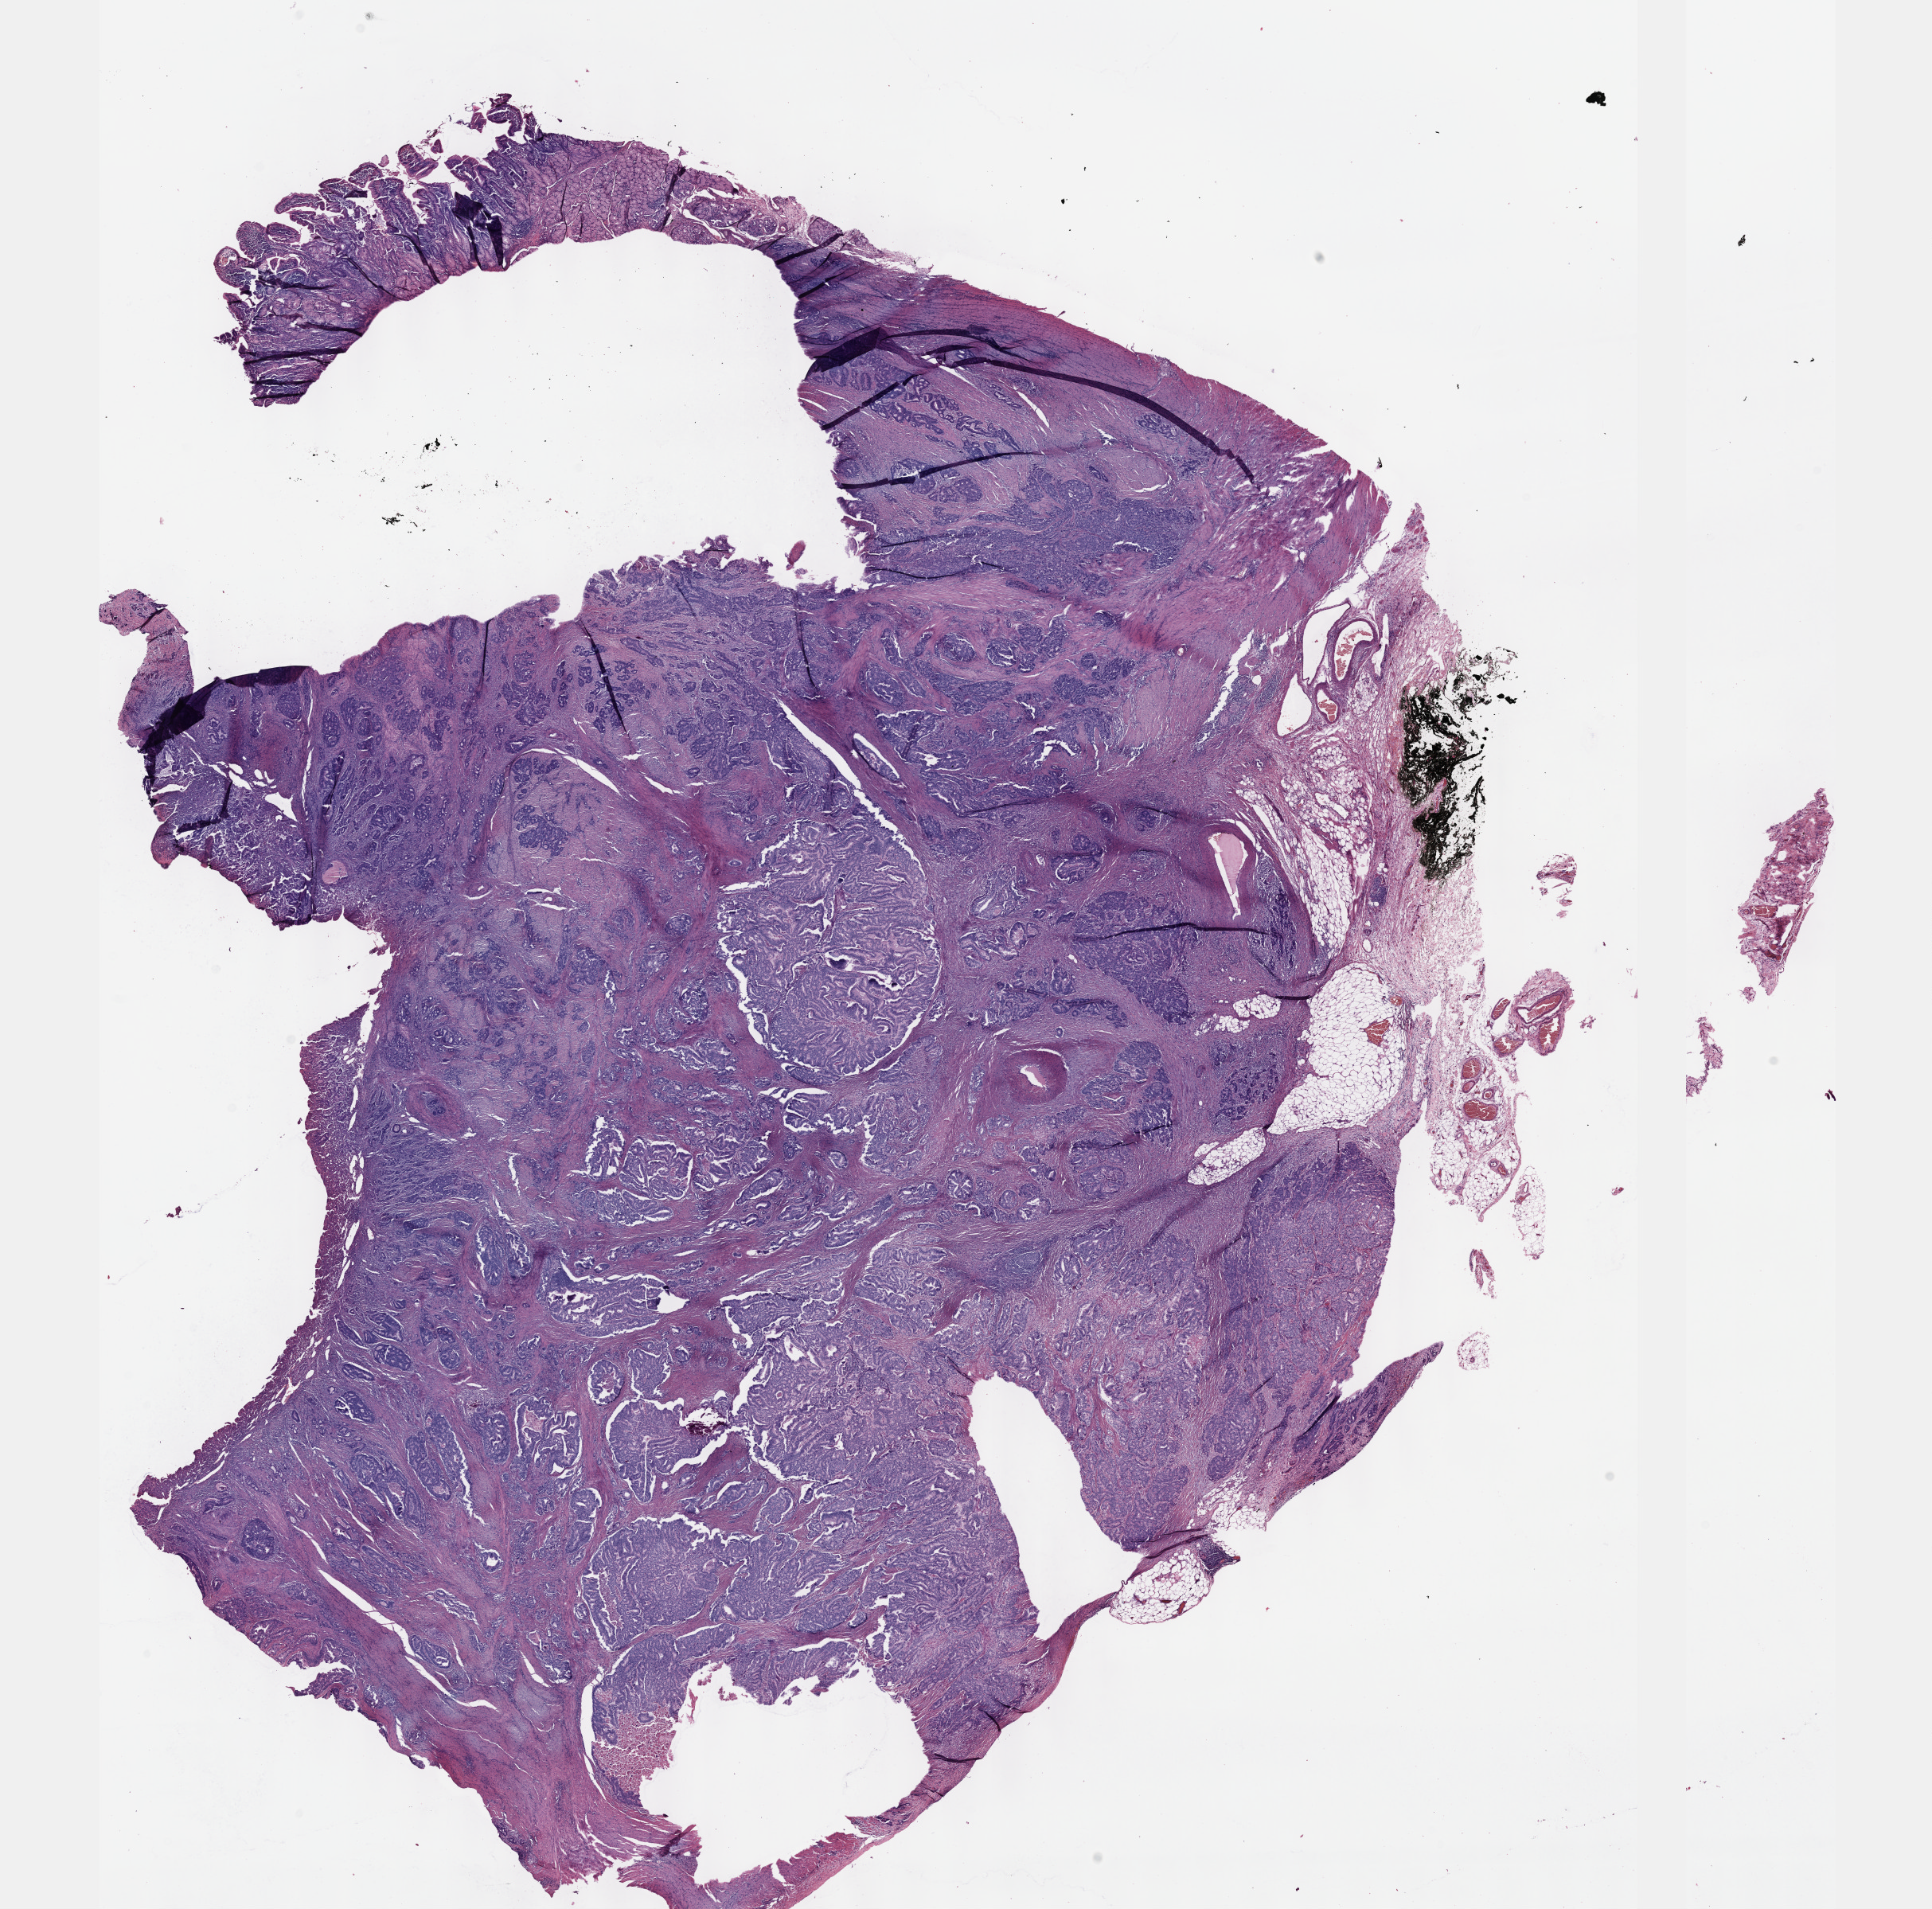
Digitized H&E-stained tissue section (whole slide) — low-resolution overview of the scanned area, about 19.6 x 19.4 mm. FFPE section. Sample: primary tumour, stomach. Male, age 63 years at initial diagnosis. Histologic grade: G2 (moderately differentiated).
Histologic diagnosis: Adenocarcinoma, intestinal type (gastric antrum). Lymph nodes positive (case pathology): 6 of 32 examined.